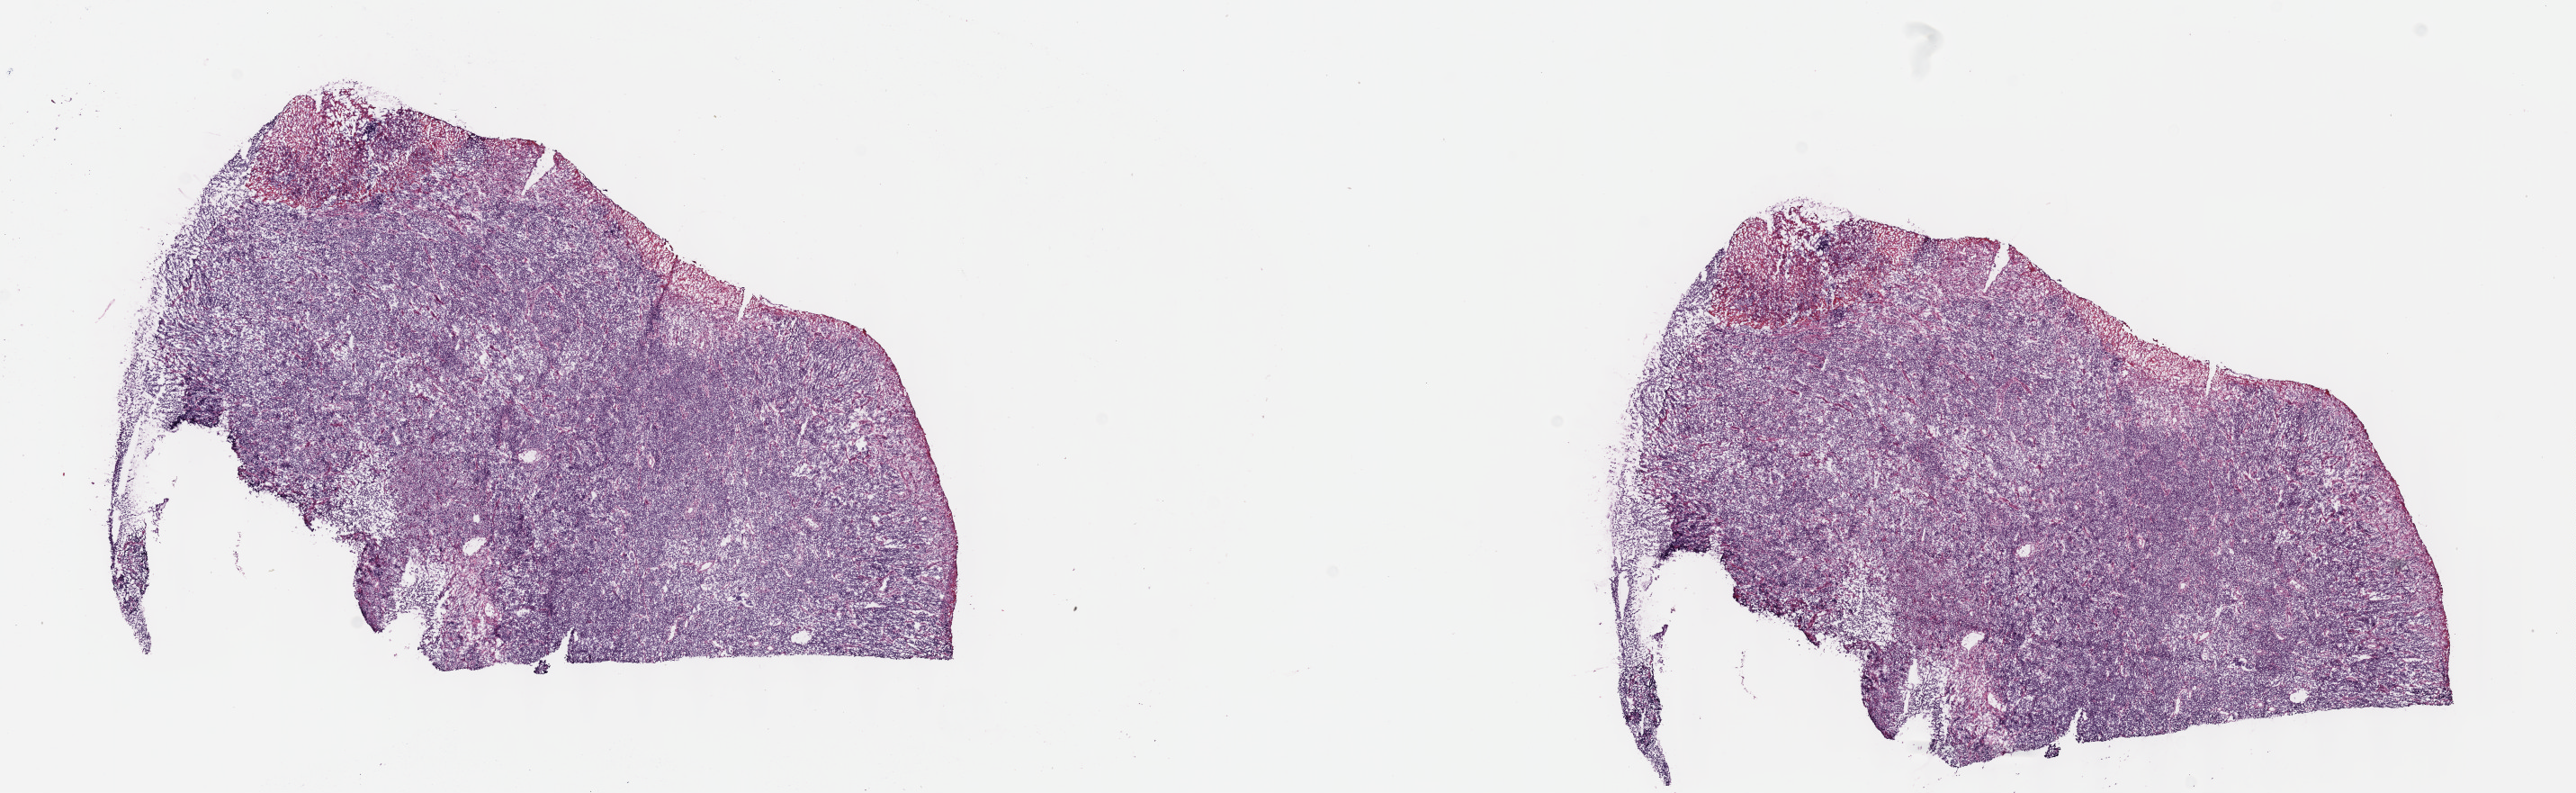
Whole-slide image, hematoxylin and eosin (H&E) stain — a low-resolution overview of the entire scanned area, about 23.1 x 7.1 mm, cryosection, specimen: primary tumor, anatomic site: cranium. Female patient; age at initial diagnosis 6 years. Composition of this section per pathologist review: tumor cells 85%, tumor nuclei 90%, stromal cells 10%, necrosis 5%, normal cells 0%. Infiltration values recorded for this section: lymphocyte infiltration 10%, monocyte infiltration 15%, neutrophil infiltration 5%.
* Ann Arbor stage (patient): Stage III
* histologic diagnosis: Burkitt lymphoma, NOS
* section: bottom of the tissue portion